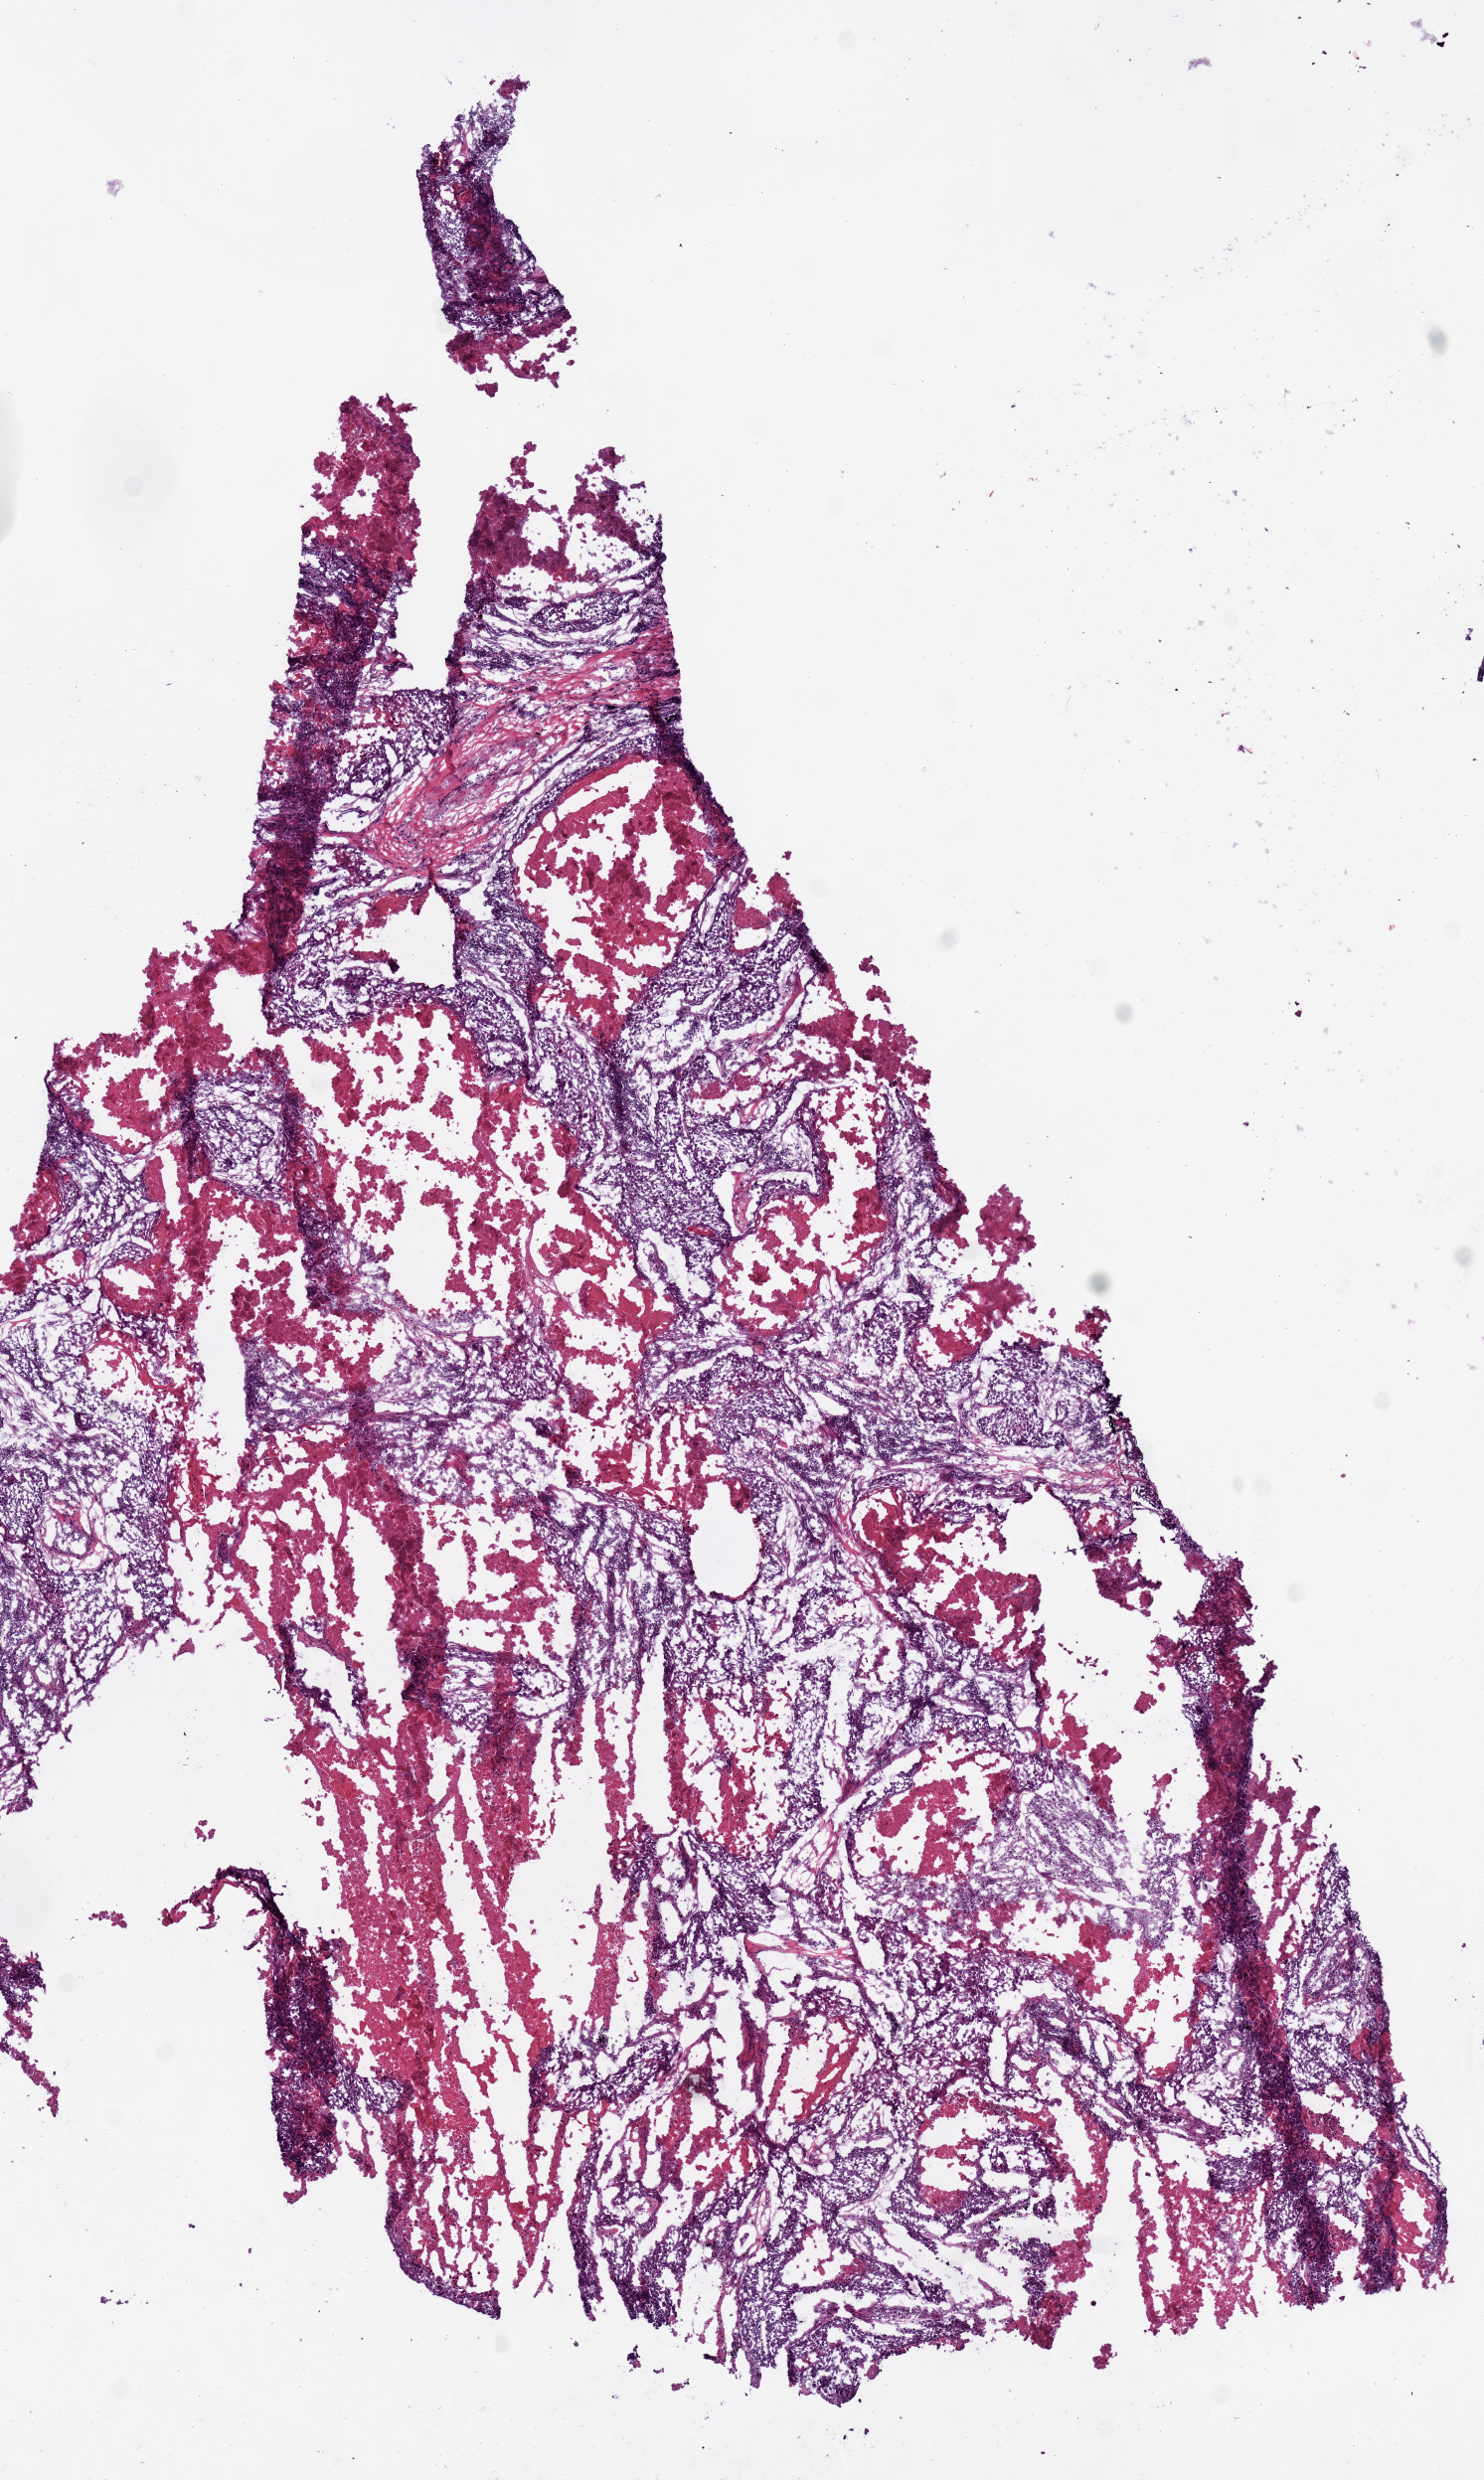
Digitized H&E tissue section (whole slide) — a low-resolution overview of the entire scanned area, about 5.9 x 9.9 mm (from a 20x scan), frozen section from the top of the tissue portion, primary tumour sample from the lung. Male patient; age at initial diagnosis 70 years. Pathologist review of this section (percent, as recorded): tumour cells 95%, tumour nuclei 70%, normal cells 0%, stromal cells 0%, necrosis 5%. Inflammatory infiltration, as recorded: lymphocyte infiltration 20%, monocyte infiltration 0%, neutrophil infiltration 0%.
AJCC pathologic stage: IIIA (7th edition). Histologic diagnosis: Squamous cell carcinoma, NOS (upper lobe, lung). Laterality: left.